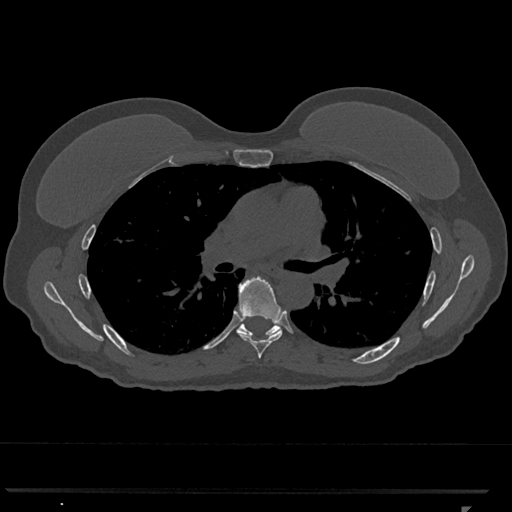
CT including the spine, one axial slice. Position 745 of 793 along the scan axis. Reconstruction kernel Br40s/3. 120 kVp. Bone window (W 1800 / L 400 HU). 512 × 512 image matrix, field of view 380 × 380 mm. Female patient, age 62 years. Case-level facts recorded for this patient, not image findings: primary cancer: renal.
Annotated regions visible in this slice (semi-automatically segmented with operator editing):
- T6 vertebra: bounding box [x1, y1, x2, y2] px = [238, 275, 283, 359]
- T7 vertebra: [237, 322, 280, 337]